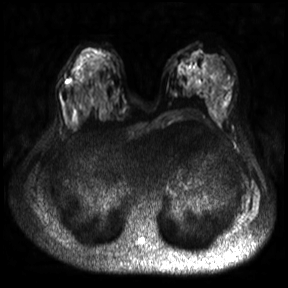
Breast MRI, one axial slice. Slice 15 of 30 in the series (ordered by position). Diffusion-weighted series; image 2 of 4 stored at this slice position (different b-values; order by instance number). 3 T. 4 mm slice thickness. 288 × 288 image matrix, field of view 360 × 360 mm. Female patient.
Outlined on this slice (manually delineated by an expert):
- tumour on diffusion-weighted imaging: bounding box <67,78,72,84> (left, top, right, bottom; pixels)